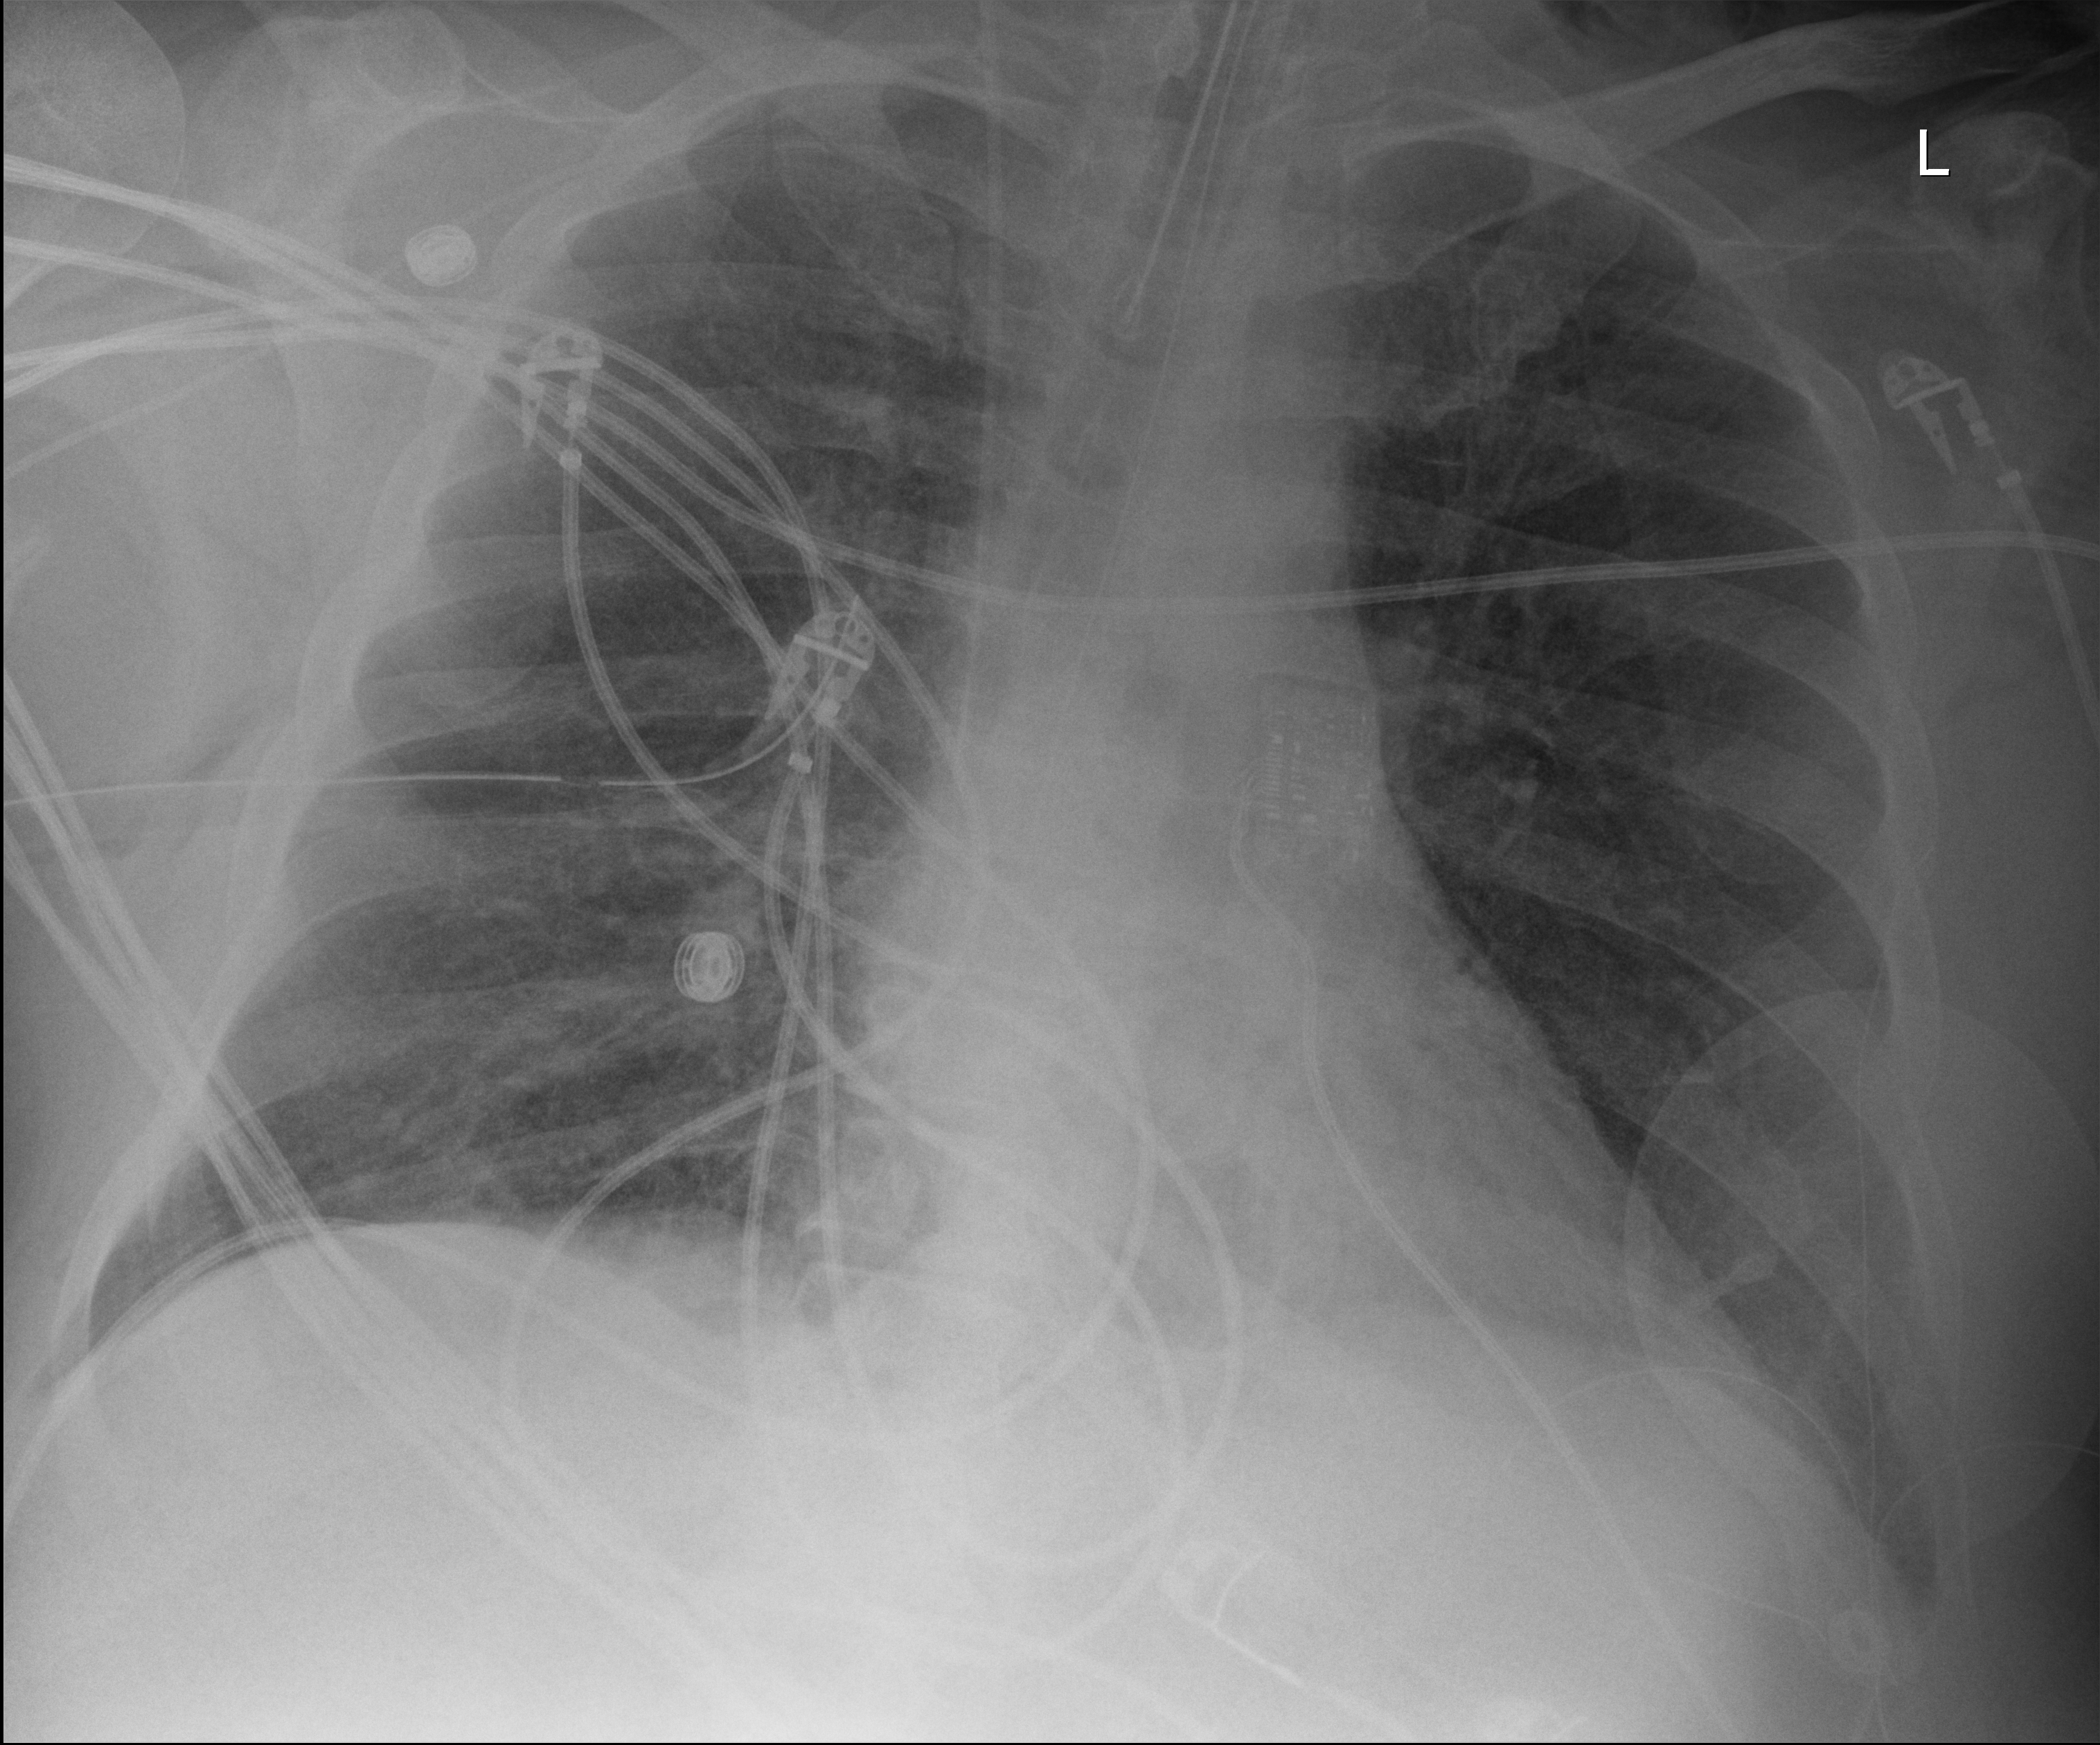
Portable chest radiograph; anteroposterior (AP) projection. Adult patient hospitalised with COVID-19, age 18–59 years.
From the hospital-stay record, not from the radiograph (when in the stay this image was taken is not recorded):
- mechanically ventilated during this hospital stay: yes